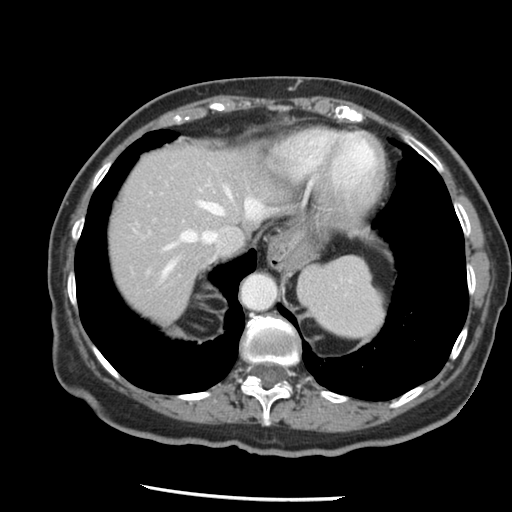
Contrast-enhanced abdominal CT, one axial slice; slice 112 of 148 in the series (ordered by position); reconstruction kernel STANDARD; 120 kVp; intravenous contrast given; soft-tissue window (W 400 / L 40 HU); 2.5 mm slice thickness; 512 × 512 image matrix. Female patient, age 85 years. From the clinical record (not read from this slice): diagnosis: colorectal cancer liver metastases, imaged before liver resection; multiple liver metastases: no; largest metastasis: 0.9 cm; disease in both lobes: no.
Annotated regions visible in this slice (manually delineated by an expert):
- hepatic veins: bounding box <163,187,262,276> (left, top, right, bottom; pixels)
- liver: <107,142,288,324>
- planned liver remnant (the part of the liver to remain after resection): <107,142,288,324>